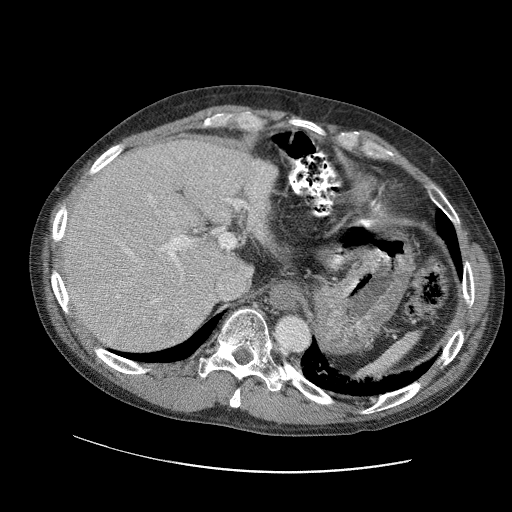
Contrast-enhanced abdominal CT (liver protocol), one axial slice; slice 76 of 109 in the series (ordered by position); reconstruction kernel STANDARD; 120 kVp; soft-tissue window (W 400 / L 40 HU); 2.5 mm slice thickness; 512 × 512 image matrix, field of view 400 × 400 mm. Case-level facts recorded for this patient, not image findings: diagnosis: hepatocellular carcinoma (patient treated with transarterial chemoembolisation; whether this scan precedes or follows treatment is not stated here); TNM stage (as recorded): Stage-IIIC; Child-Pugh class: B; tumour differentiation: well differentiated.
Annotated regions visible in this slice (semi-automatically segmented with operator editing):
- abdominal aorta: bounding box (x1, y1, x2, y2) in pixels: (277, 315, 310, 351)
- liver parenchyma outside the tumour (the mass and vessels are separate outlines, so this box may not span the whole liver): (57, 136, 275, 352)
- liver vessels: (64, 150, 262, 323)